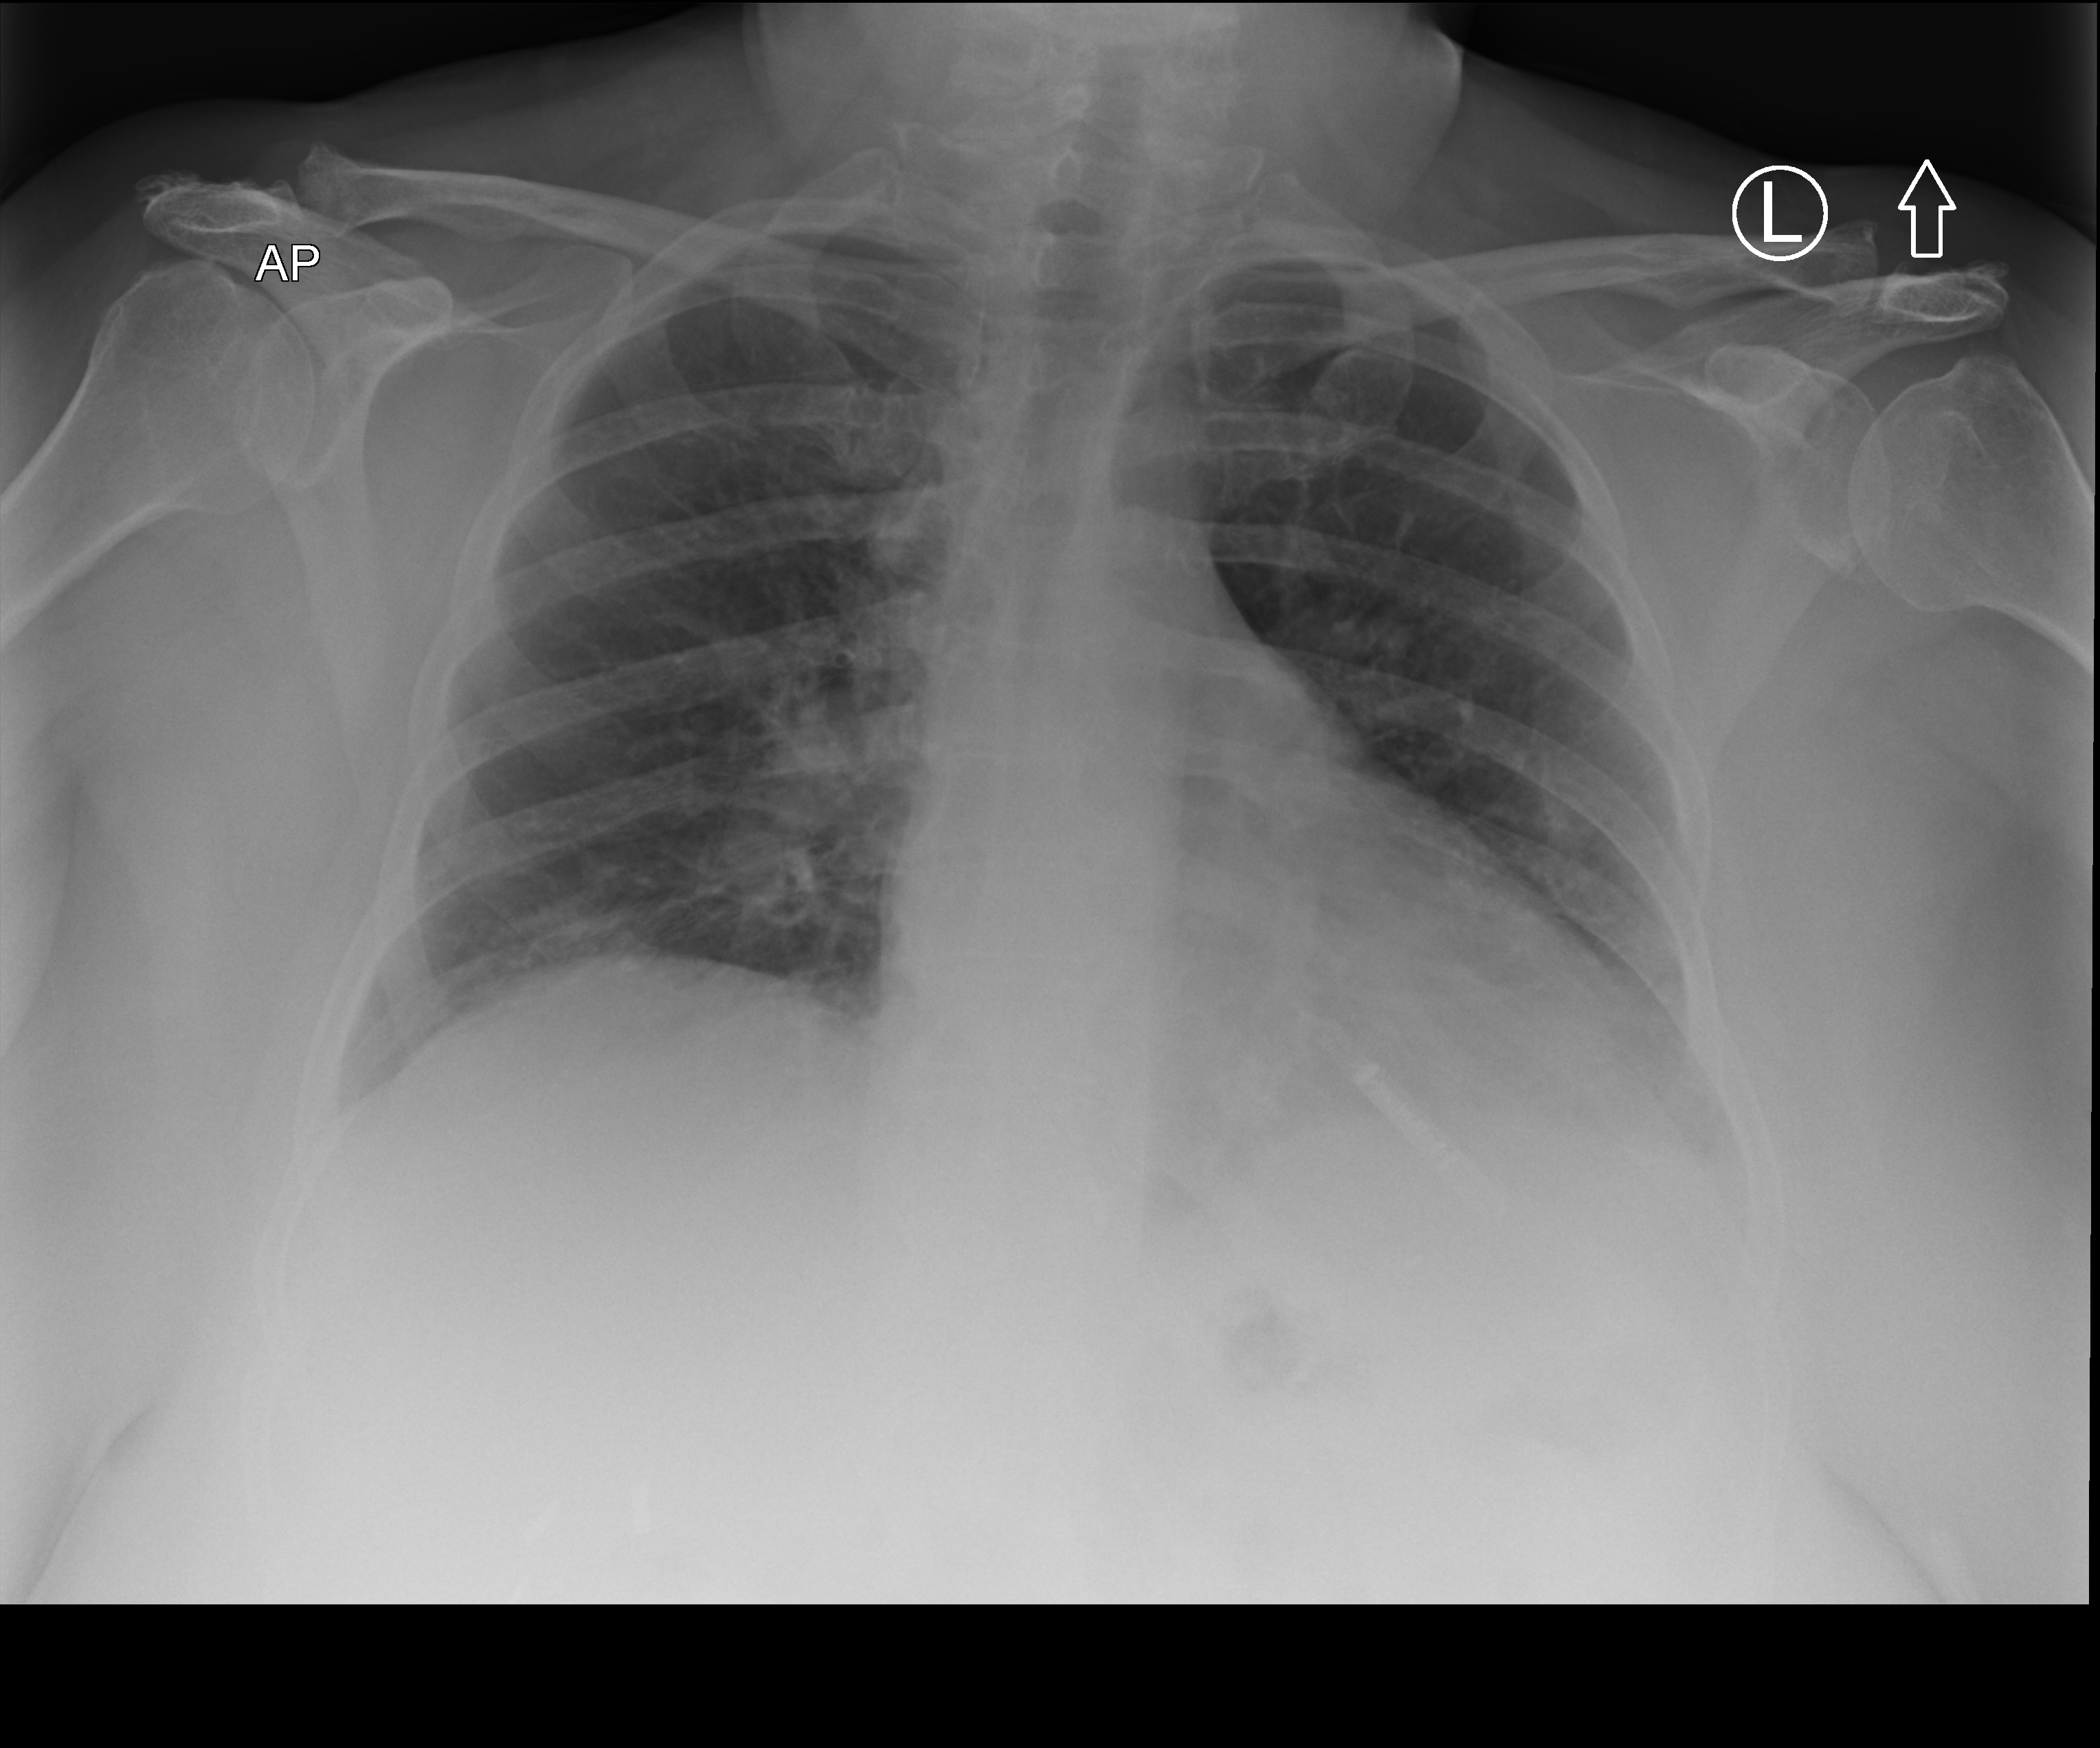
Portable chest radiograph; anteroposterior (AP) projection. Female patient hospitalised with COVID-19, age 60–74 years.
From the hospital-stay record, not from the radiograph (when in the stay this image was taken is not recorded): diabetes (admission record): no; mechanically ventilated during this hospital stay: no.